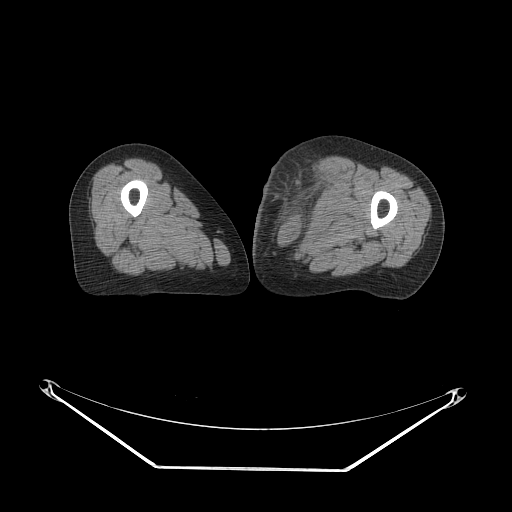
CT of an extremity soft-tissue mass (from a PET/CT study), one axial slice; position 44 of 91 along the scan axis; soft-tissue window (W 400 / L 40 HU); 512 × 512 image matrix, field of view 500 × 500 mm. Female patient. Case-level facts recorded for this patient, not image findings: histological type: pleomorphic leiomyosarcoma; grade: high; site of the primary tumour: left thigh.
Annotated regions visible in this slice (expert contour drawn on MRI and transferred to this co-registered scan by the dataset authors):
- gross tumour volume including surrounding oedema: bounding box <263,162,341,238> (left, top, right, bottom; pixels)
- gross tumour volume (mass): <290,162,330,206>